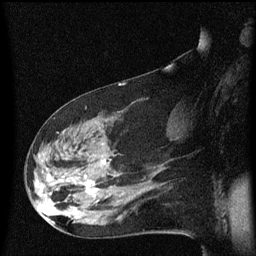
Breast MRI (dynamic contrast-enhanced), one sagittal slice; slice 33 of 60 in the series (ordered by position); dynamic contrast-enhanced series, image 2 of 3 at this slice position (ordered by acquisition); 1.5 T; TE 4.2 ms, TR 8.4 ms; 256 × 256 image matrix, field of view 200 × 200 mm. Patient: female, 48 years.
Outlined on this slice (semi-automatic segmentation, software-assisted and operator-edited):
- analysis volume of interest (the breast-tissue region the enhancement analysis was run in; not a lesion): box from (x=31, y=118) to (x=134, y=225) px
- tumour enhancement mask (voxels above the 70 % enhancement threshold inside the analysis volume of interest): (x=84, y=160)–(x=105, y=197)